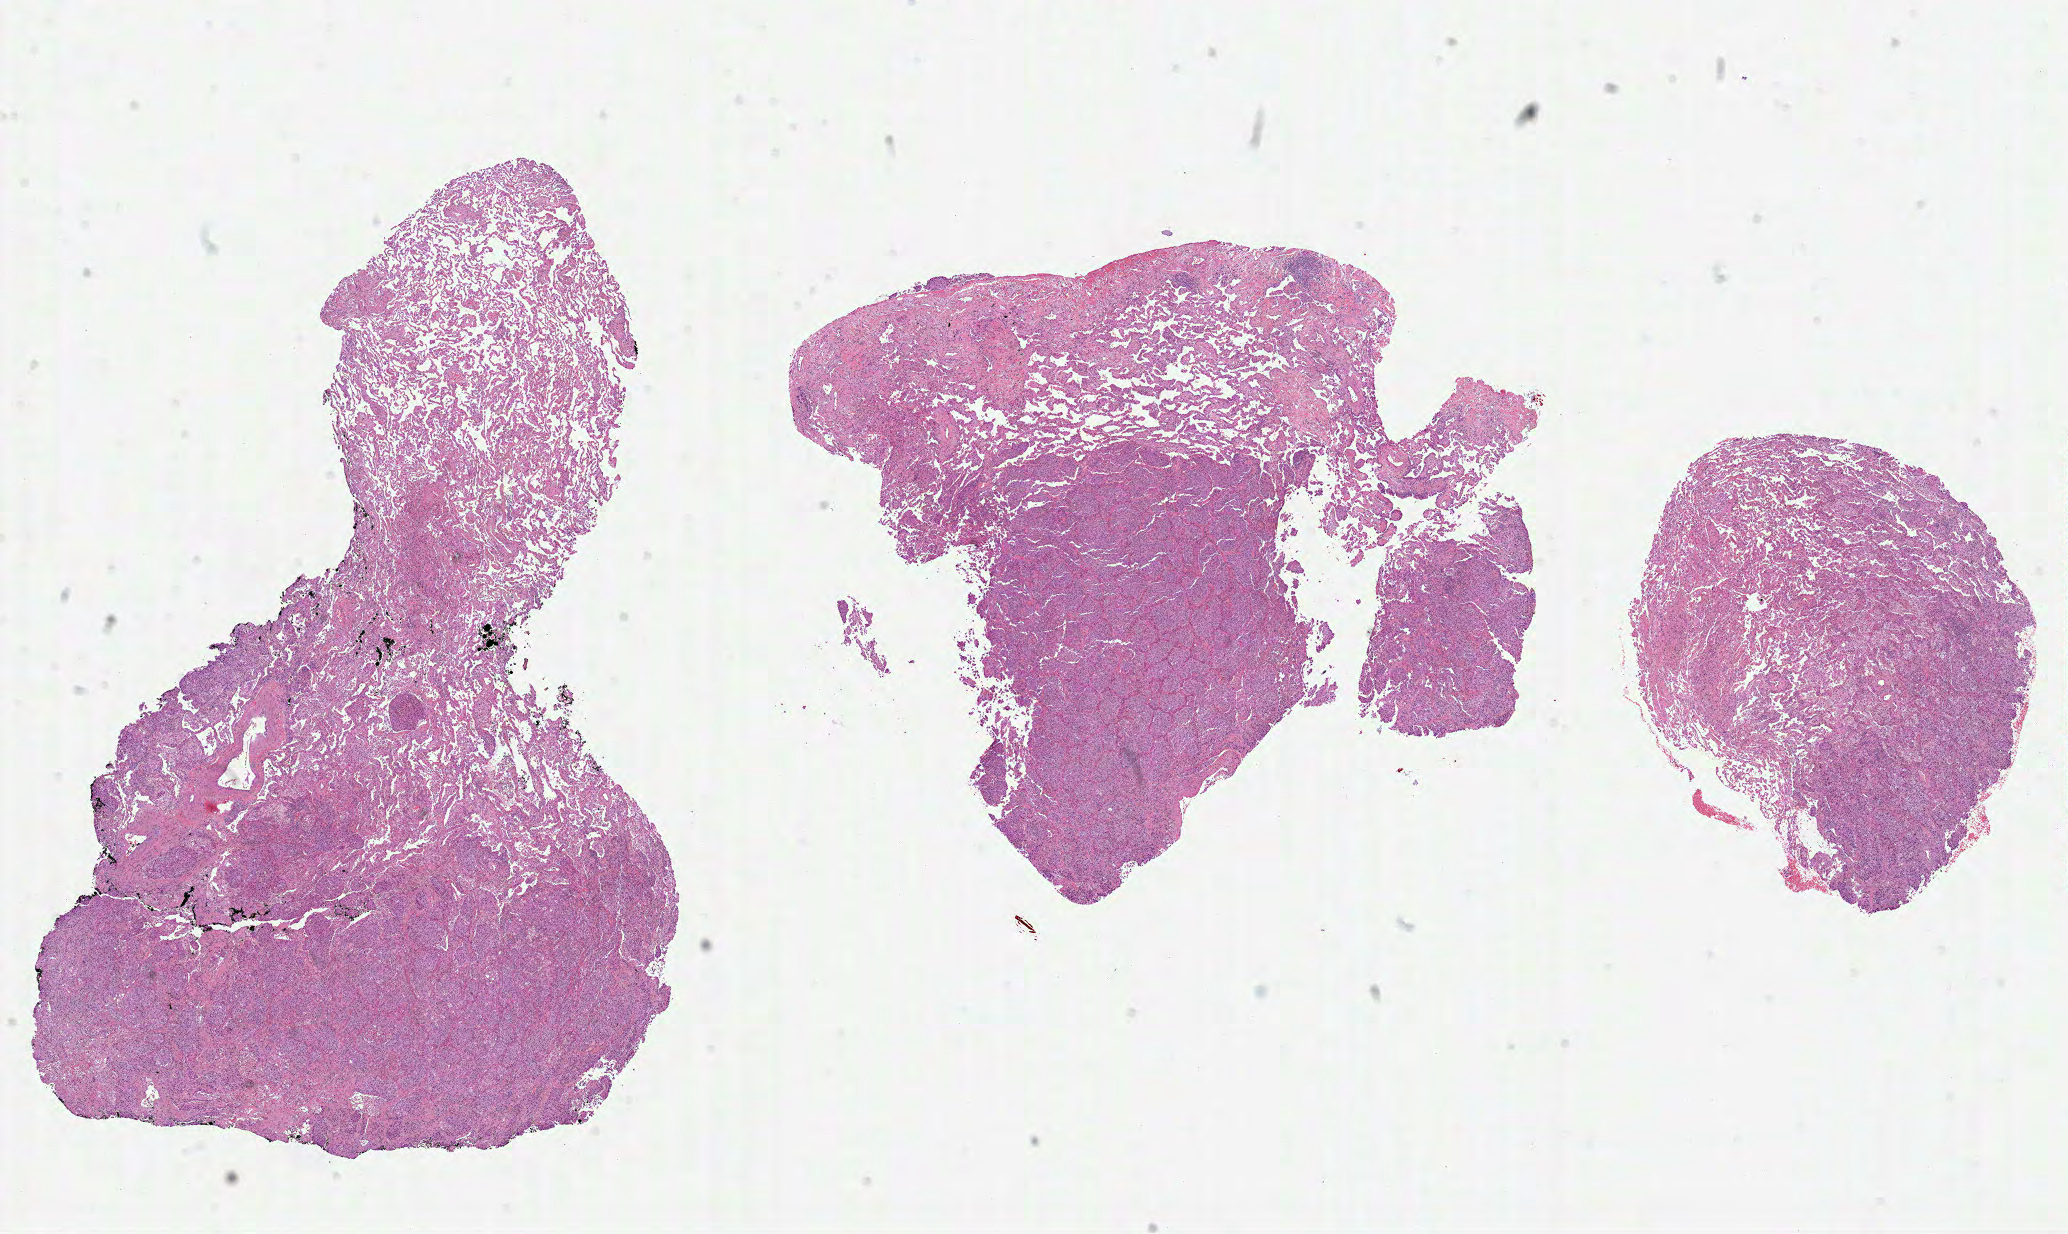
Digitized H&E tissue section (whole slide), a low-resolution overview of the entire scanned area, about 16.7 x 10.0 mm (slide scanned at 40x); formalin-fixed paraffin-embedded (FFPE) diagnostic section; primary tumour sample from the lung. Female, age 76 years at initial diagnosis.
Diagnosis: Adenocarcinoma, NOS (lower lobe, lung). AJCC pathologic stage: IIA (7th edition).